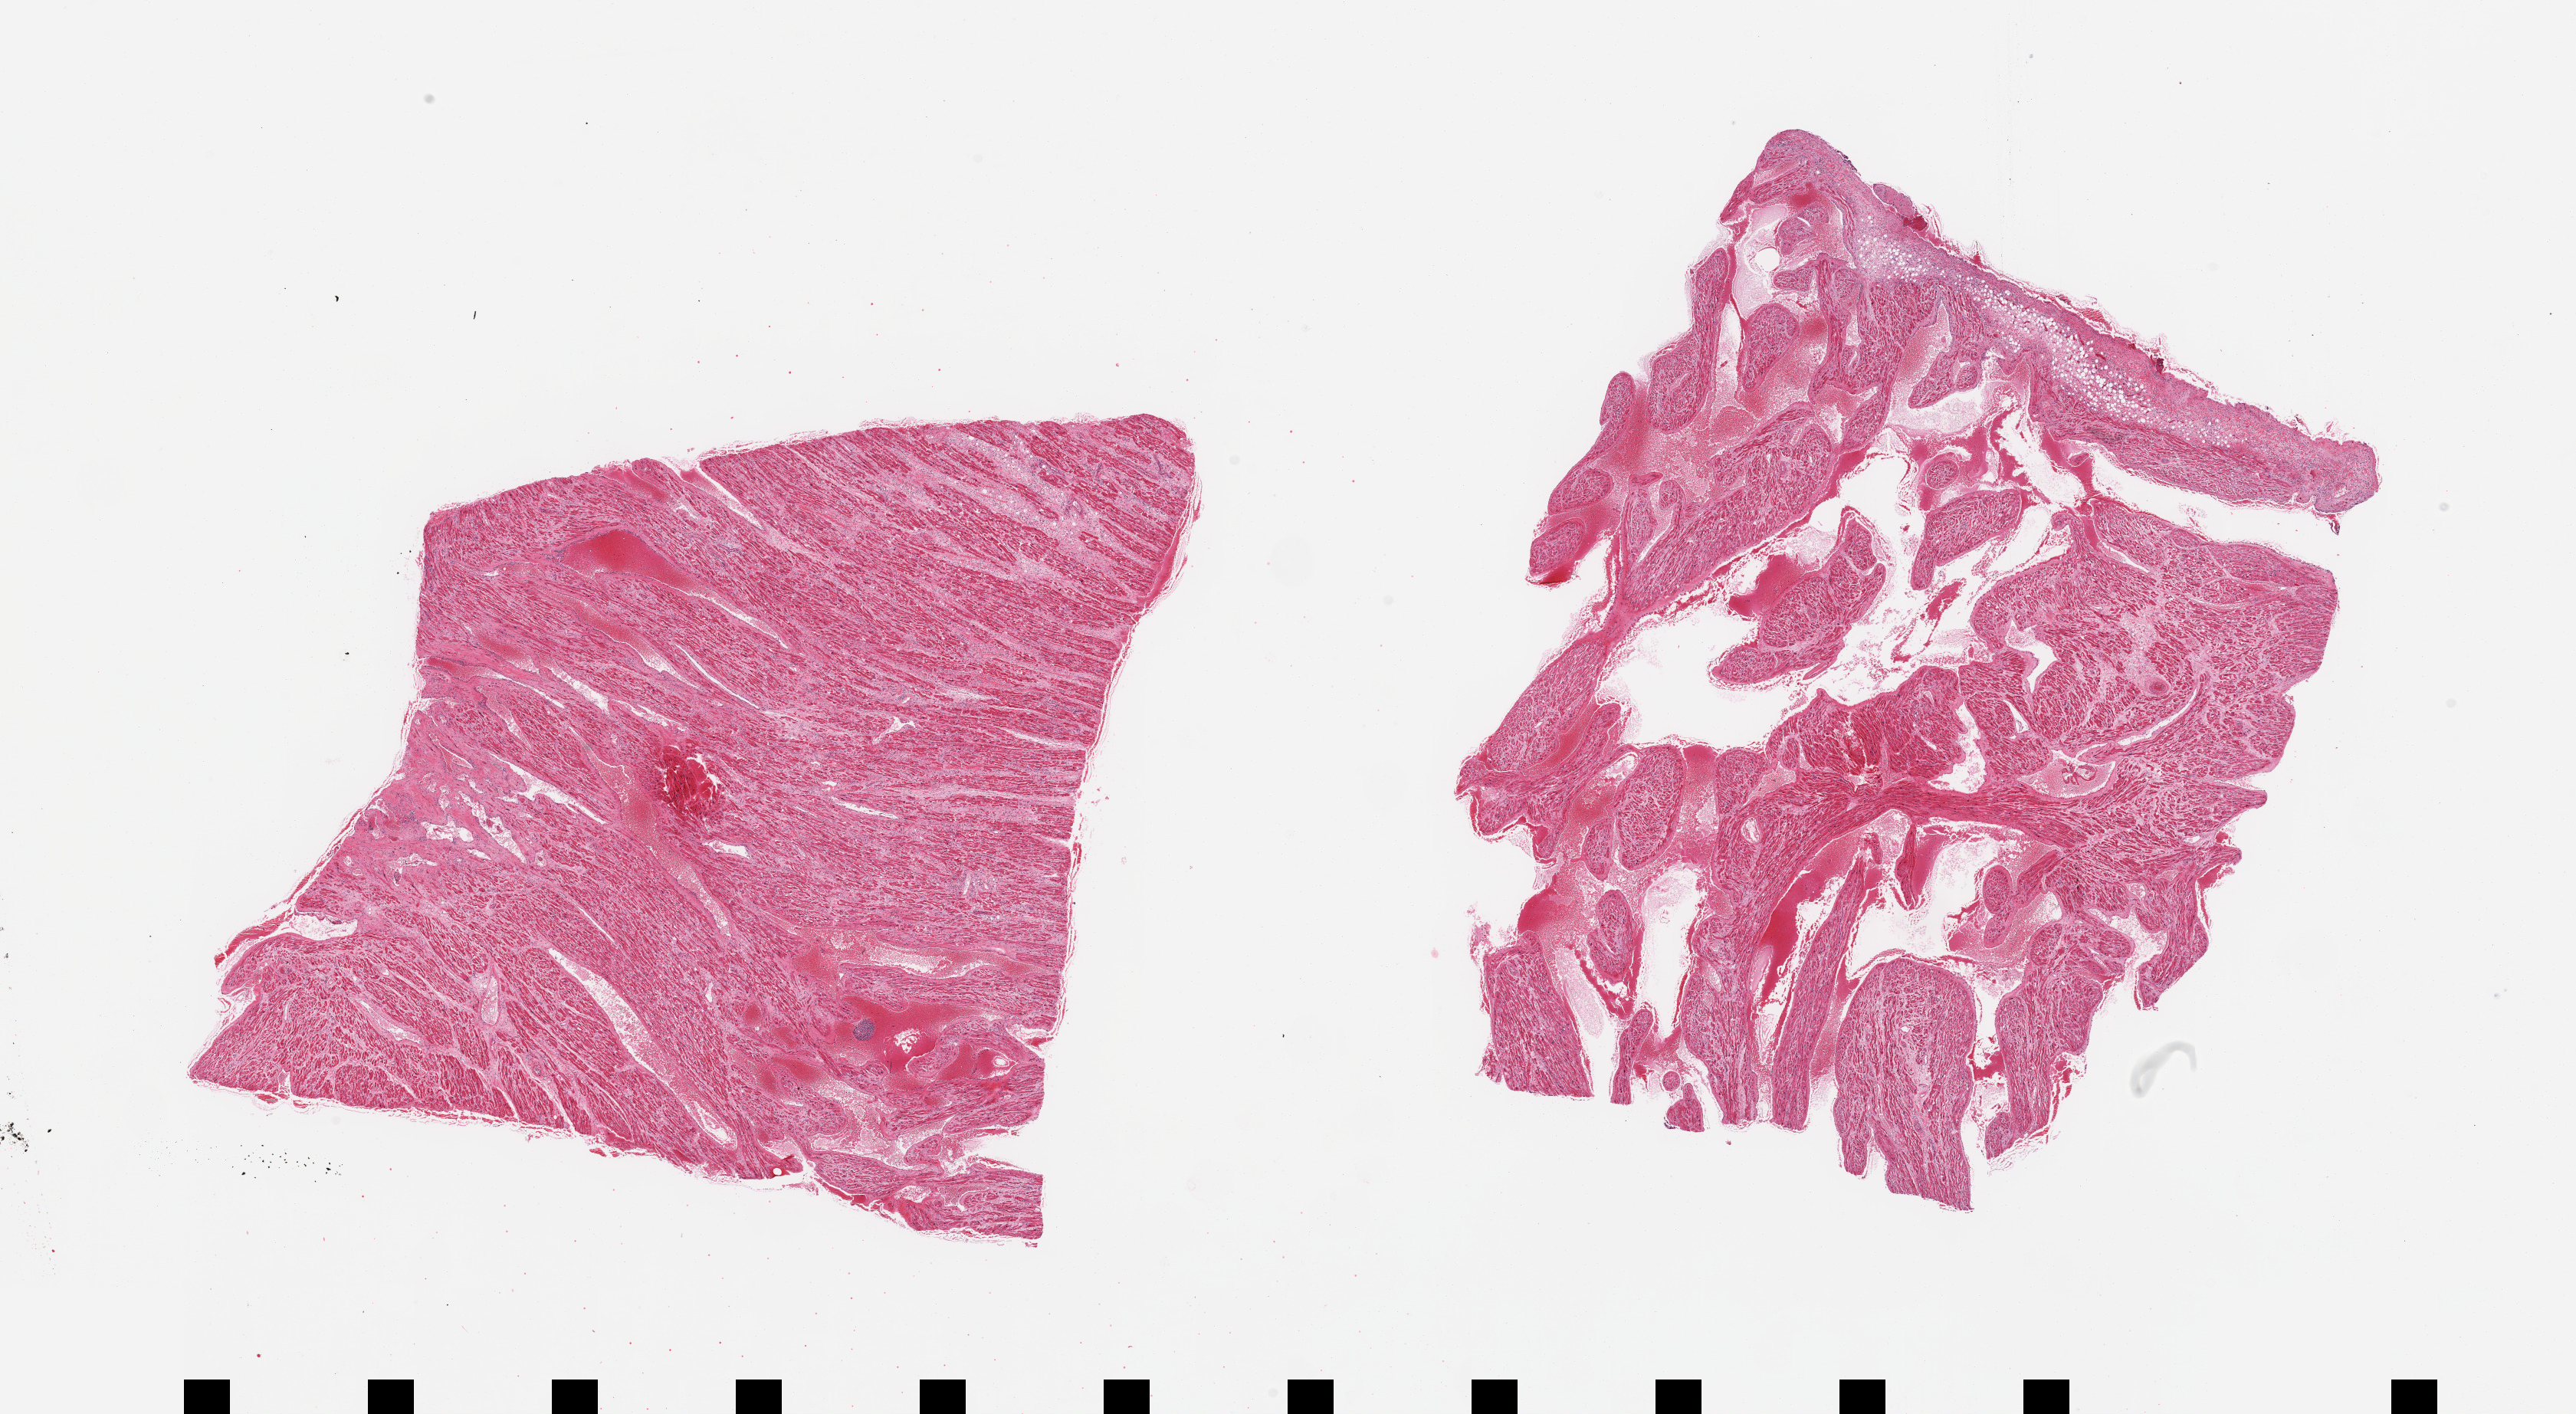
Whole-slide image, haematoxylin and eosin stain, shown as a low-resolution overview of the whole scanned area (about 26.6 x 14.6 mm, slide scanned at 20x). PAXgene-fixed, paraffin-embedded tissue. Target tissue: auricular appendage. Tissue donor sample. Male donor.
Review note (as recorded): 2 pieces; 10% peripheral fat on 1 piece; 10% blood clots.